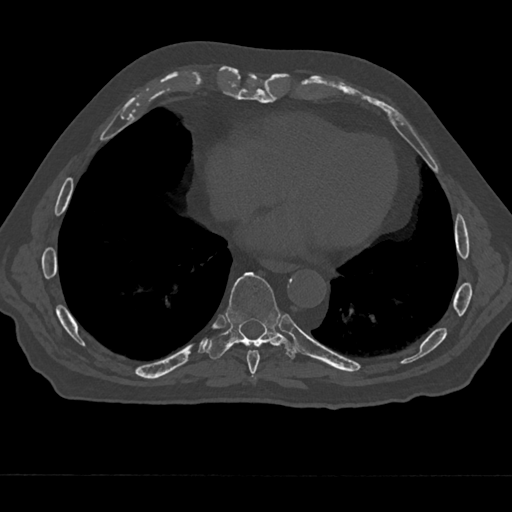
CT including the spine, one axial slice. Position 279 of 797 along the scan axis. Reconstruction kernel Br40s/3. Bone window (W 1800 / L 400 HU). 0.5 mm slice thickness. 512 × 512 image matrix. Male patient, age 75 years. From the clinical record (not read from this slice): primary cancer: renal; vertebrae with lytic lesions (as recorded): T4.
Annotated regions visible in this slice (semi-automatic segmentation, software-assisted and operator-edited):
- T8 vertebra: bounding box <246,350,260,375> (left, top, right, bottom; pixels)
- T9 vertebra: <206,272,296,359>